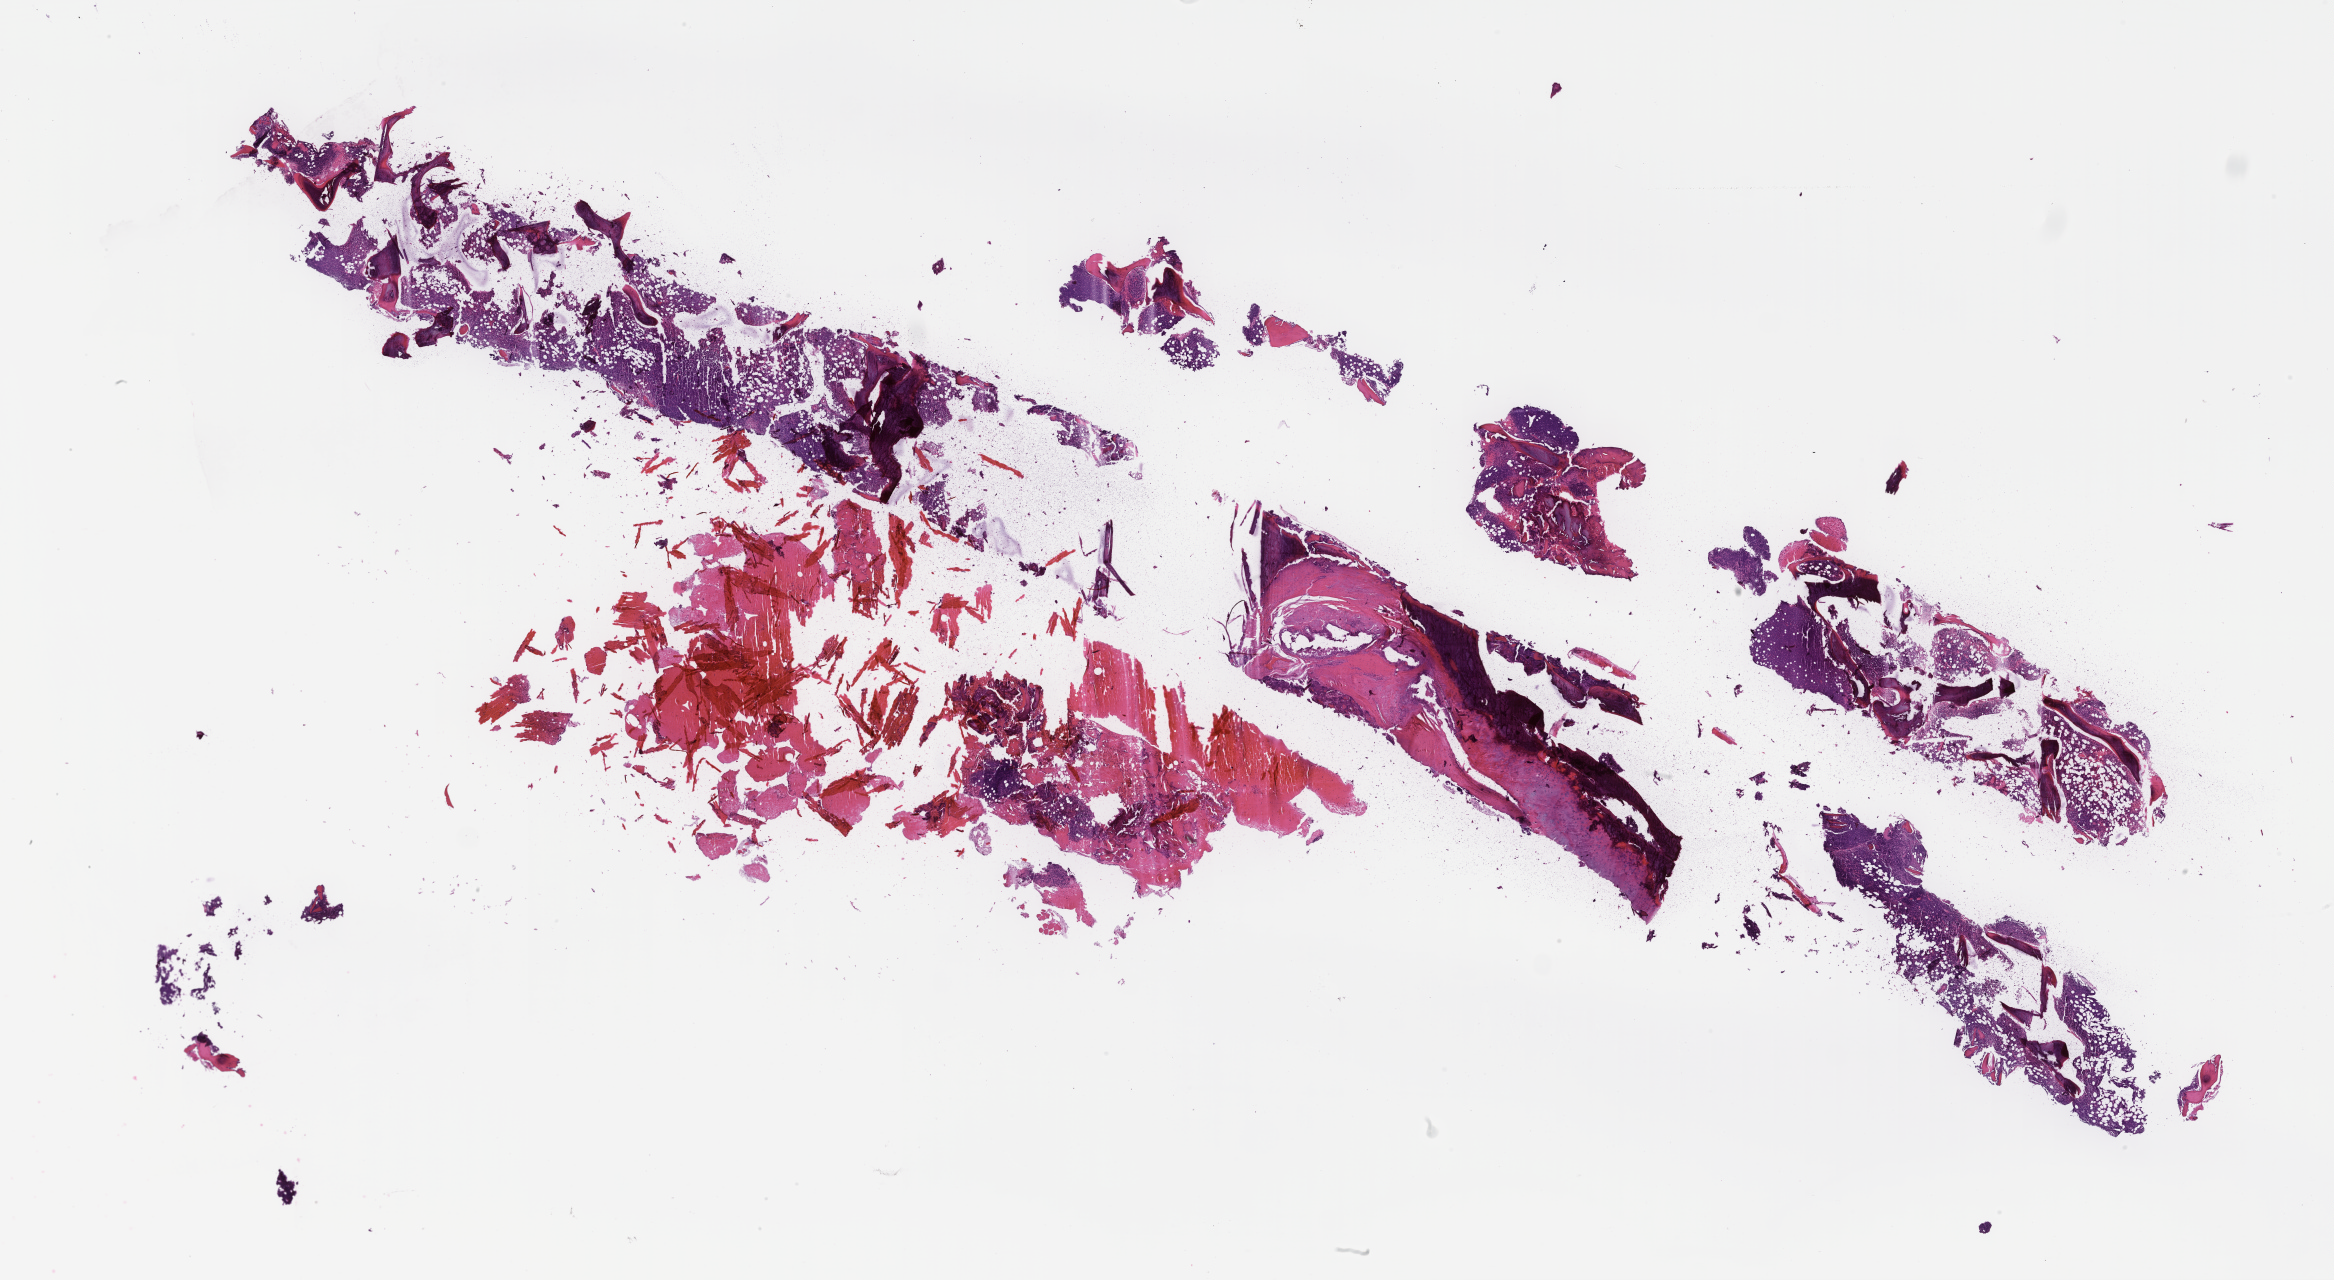
Hematoxylin and eosin (H&E) whole-slide image, low-resolution overview of the scanned area, about 37.7 x 20.7 mm; formalin-fixed, paraffin-embedded (FFPE) tissue; site: bone marrow. Patient: male.
- this section: primary tumor
- diagnosis: Plasma Cell Myeloma